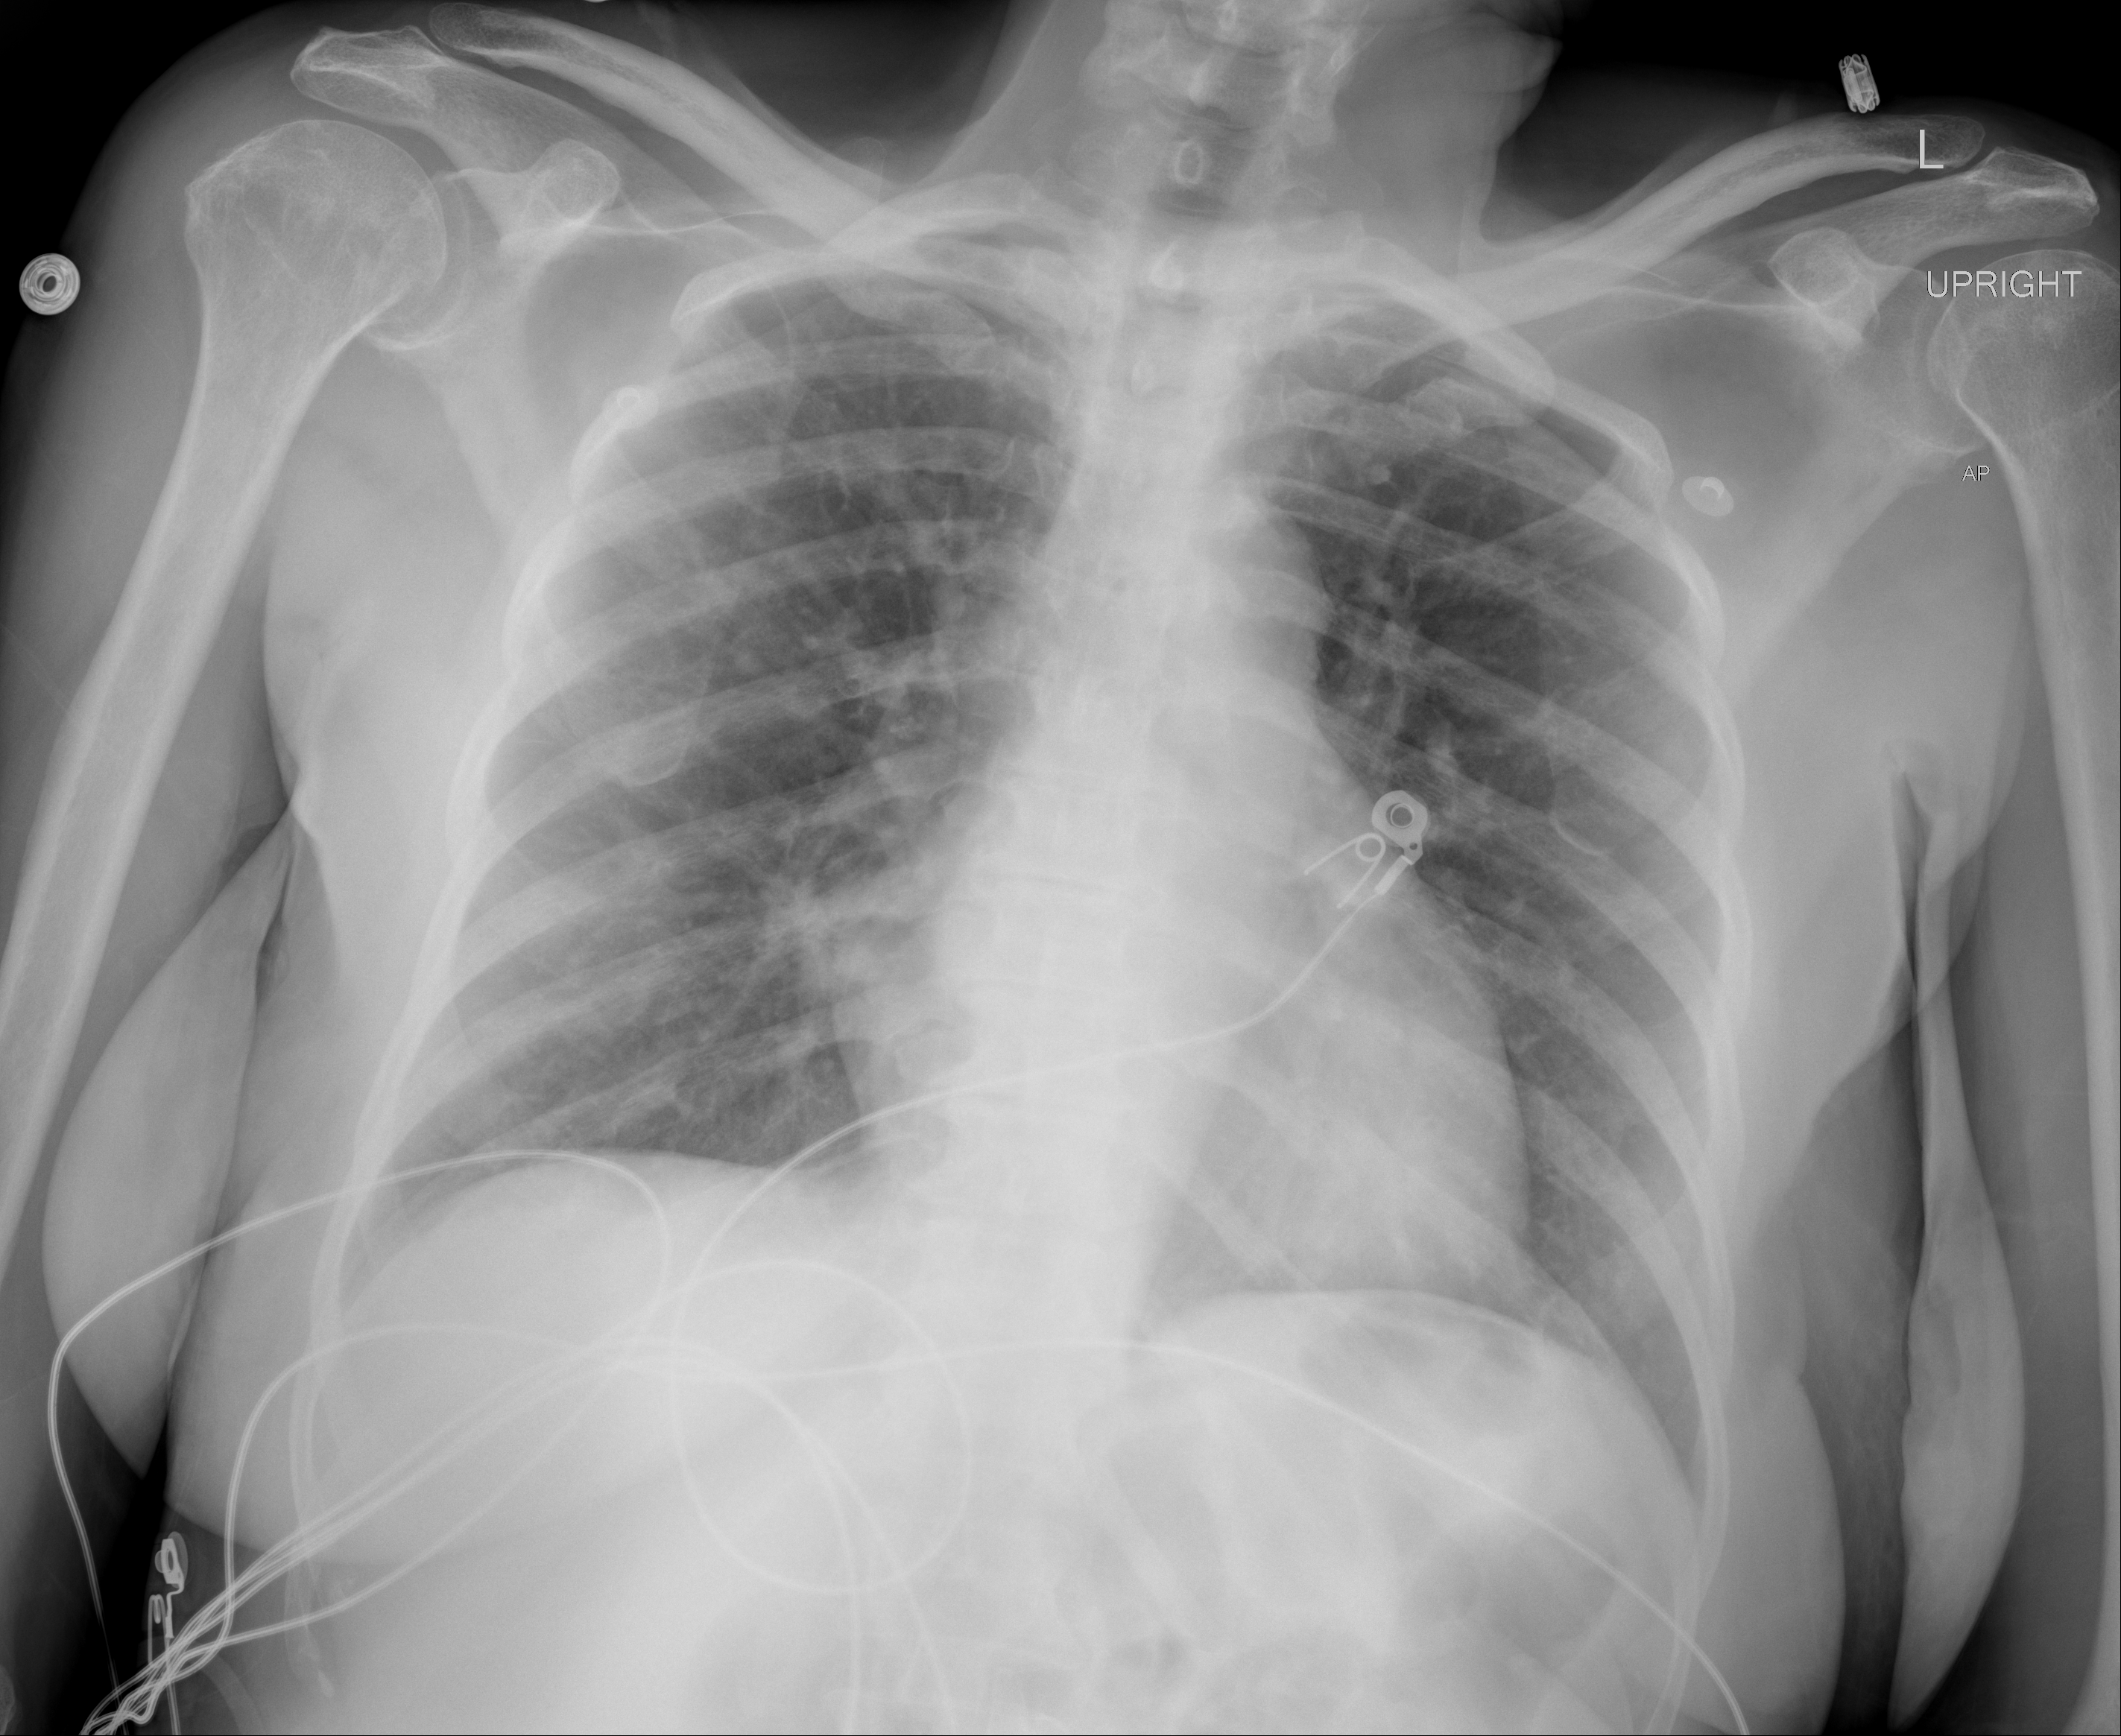
Chest radiograph, AP projection. Female patient, age 81 years; imaged 0 days after the COVID-19 diagnosis.
Radiologist key findings (as recorded): Subtle hazy opacities at both lung bases.